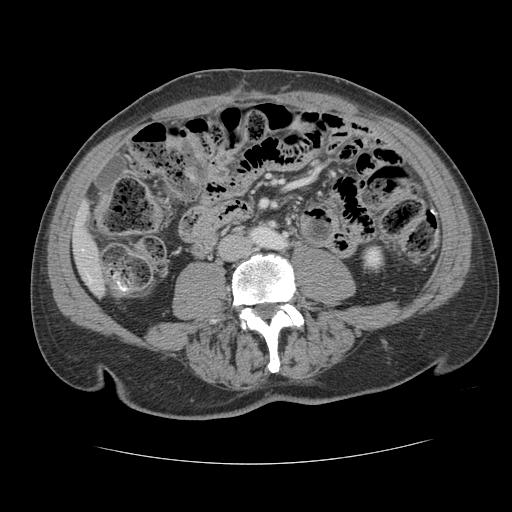
Contrast-enhanced abdominal CT, one axial slice; slice 22 of 134 in the series (ordered by position); intravenous contrast given; soft-tissue window (W 400 / L 40 HU); 512 × 512 image matrix, field of view 377 × 377 mm. Male patient, age 68 years. Case-level facts recorded for this patient, not image findings: diagnosis: colorectal cancer liver metastases, imaged before liver resection; multiple liver metastases: yes.
Annotated regions visible in this slice (expert manual segmentation):
- liver: bounding box [x1, y1, x2, y2] px = [74, 214, 104, 293]
- planned liver remnant (the part of the liver to remain after resection): [74, 216, 103, 293]